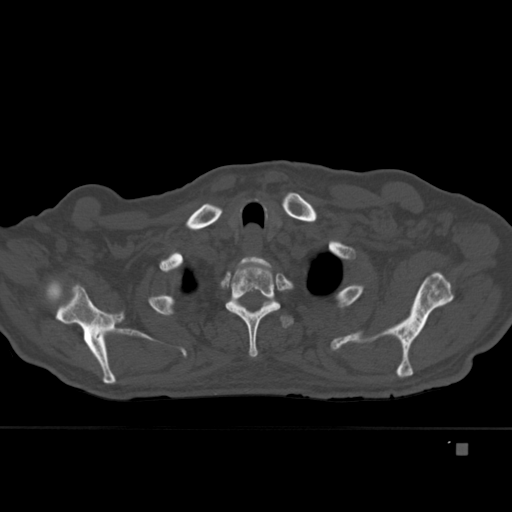
CT including the spine, one axial slice; slice 346 of 451 in the series (ordered by position); bone window (W 1800 / L 400 HU); 1.5 mm slice thickness; 512 × 512 image matrix. Male patient, age 75 years. From the clinical record (not read from this slice): primary cancer: prostate.
Annotated regions visible in this slice (semi-automatic segmentation, software-assisted and operator-edited):
- T1 vertebra: bounding box <241,256,271,267> (left, top, right, bottom; pixels)
- T2 vertebra: <225,256,281,358>
- T3 vertebra: <241,301,293,328>